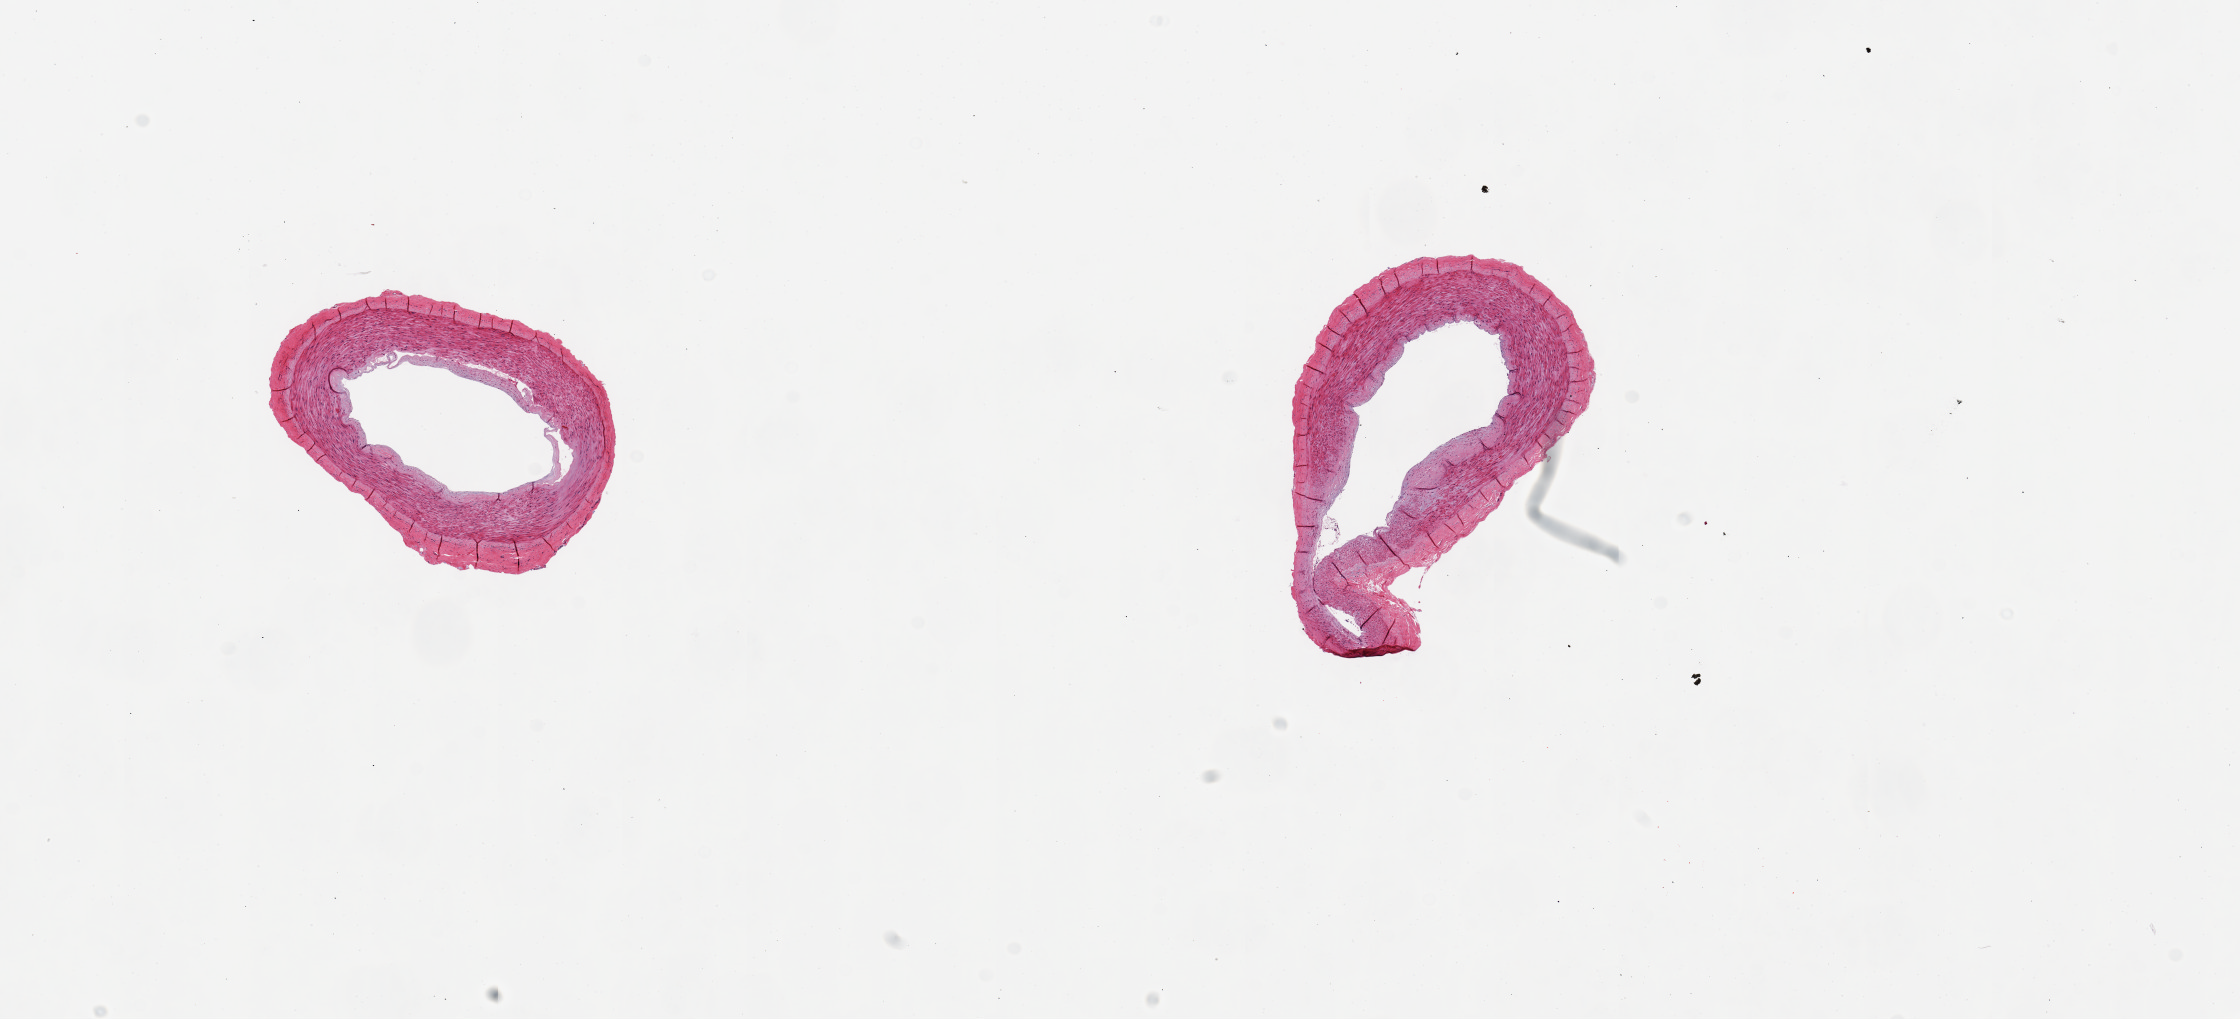
Haematoxylin and eosin whole-slide image — whole scanned area (about 17.7 x 8.1 mm) shown as a low-resolution overview, PAXgene-fixed, paraffin-embedded tissue, sampled site (target tissue): tibial artery, tissue donor sample. Donor sex: female.
Reviewer comment on this tissue sample: 2 pieces, 3x2 & 3x2mm; clean specimen.